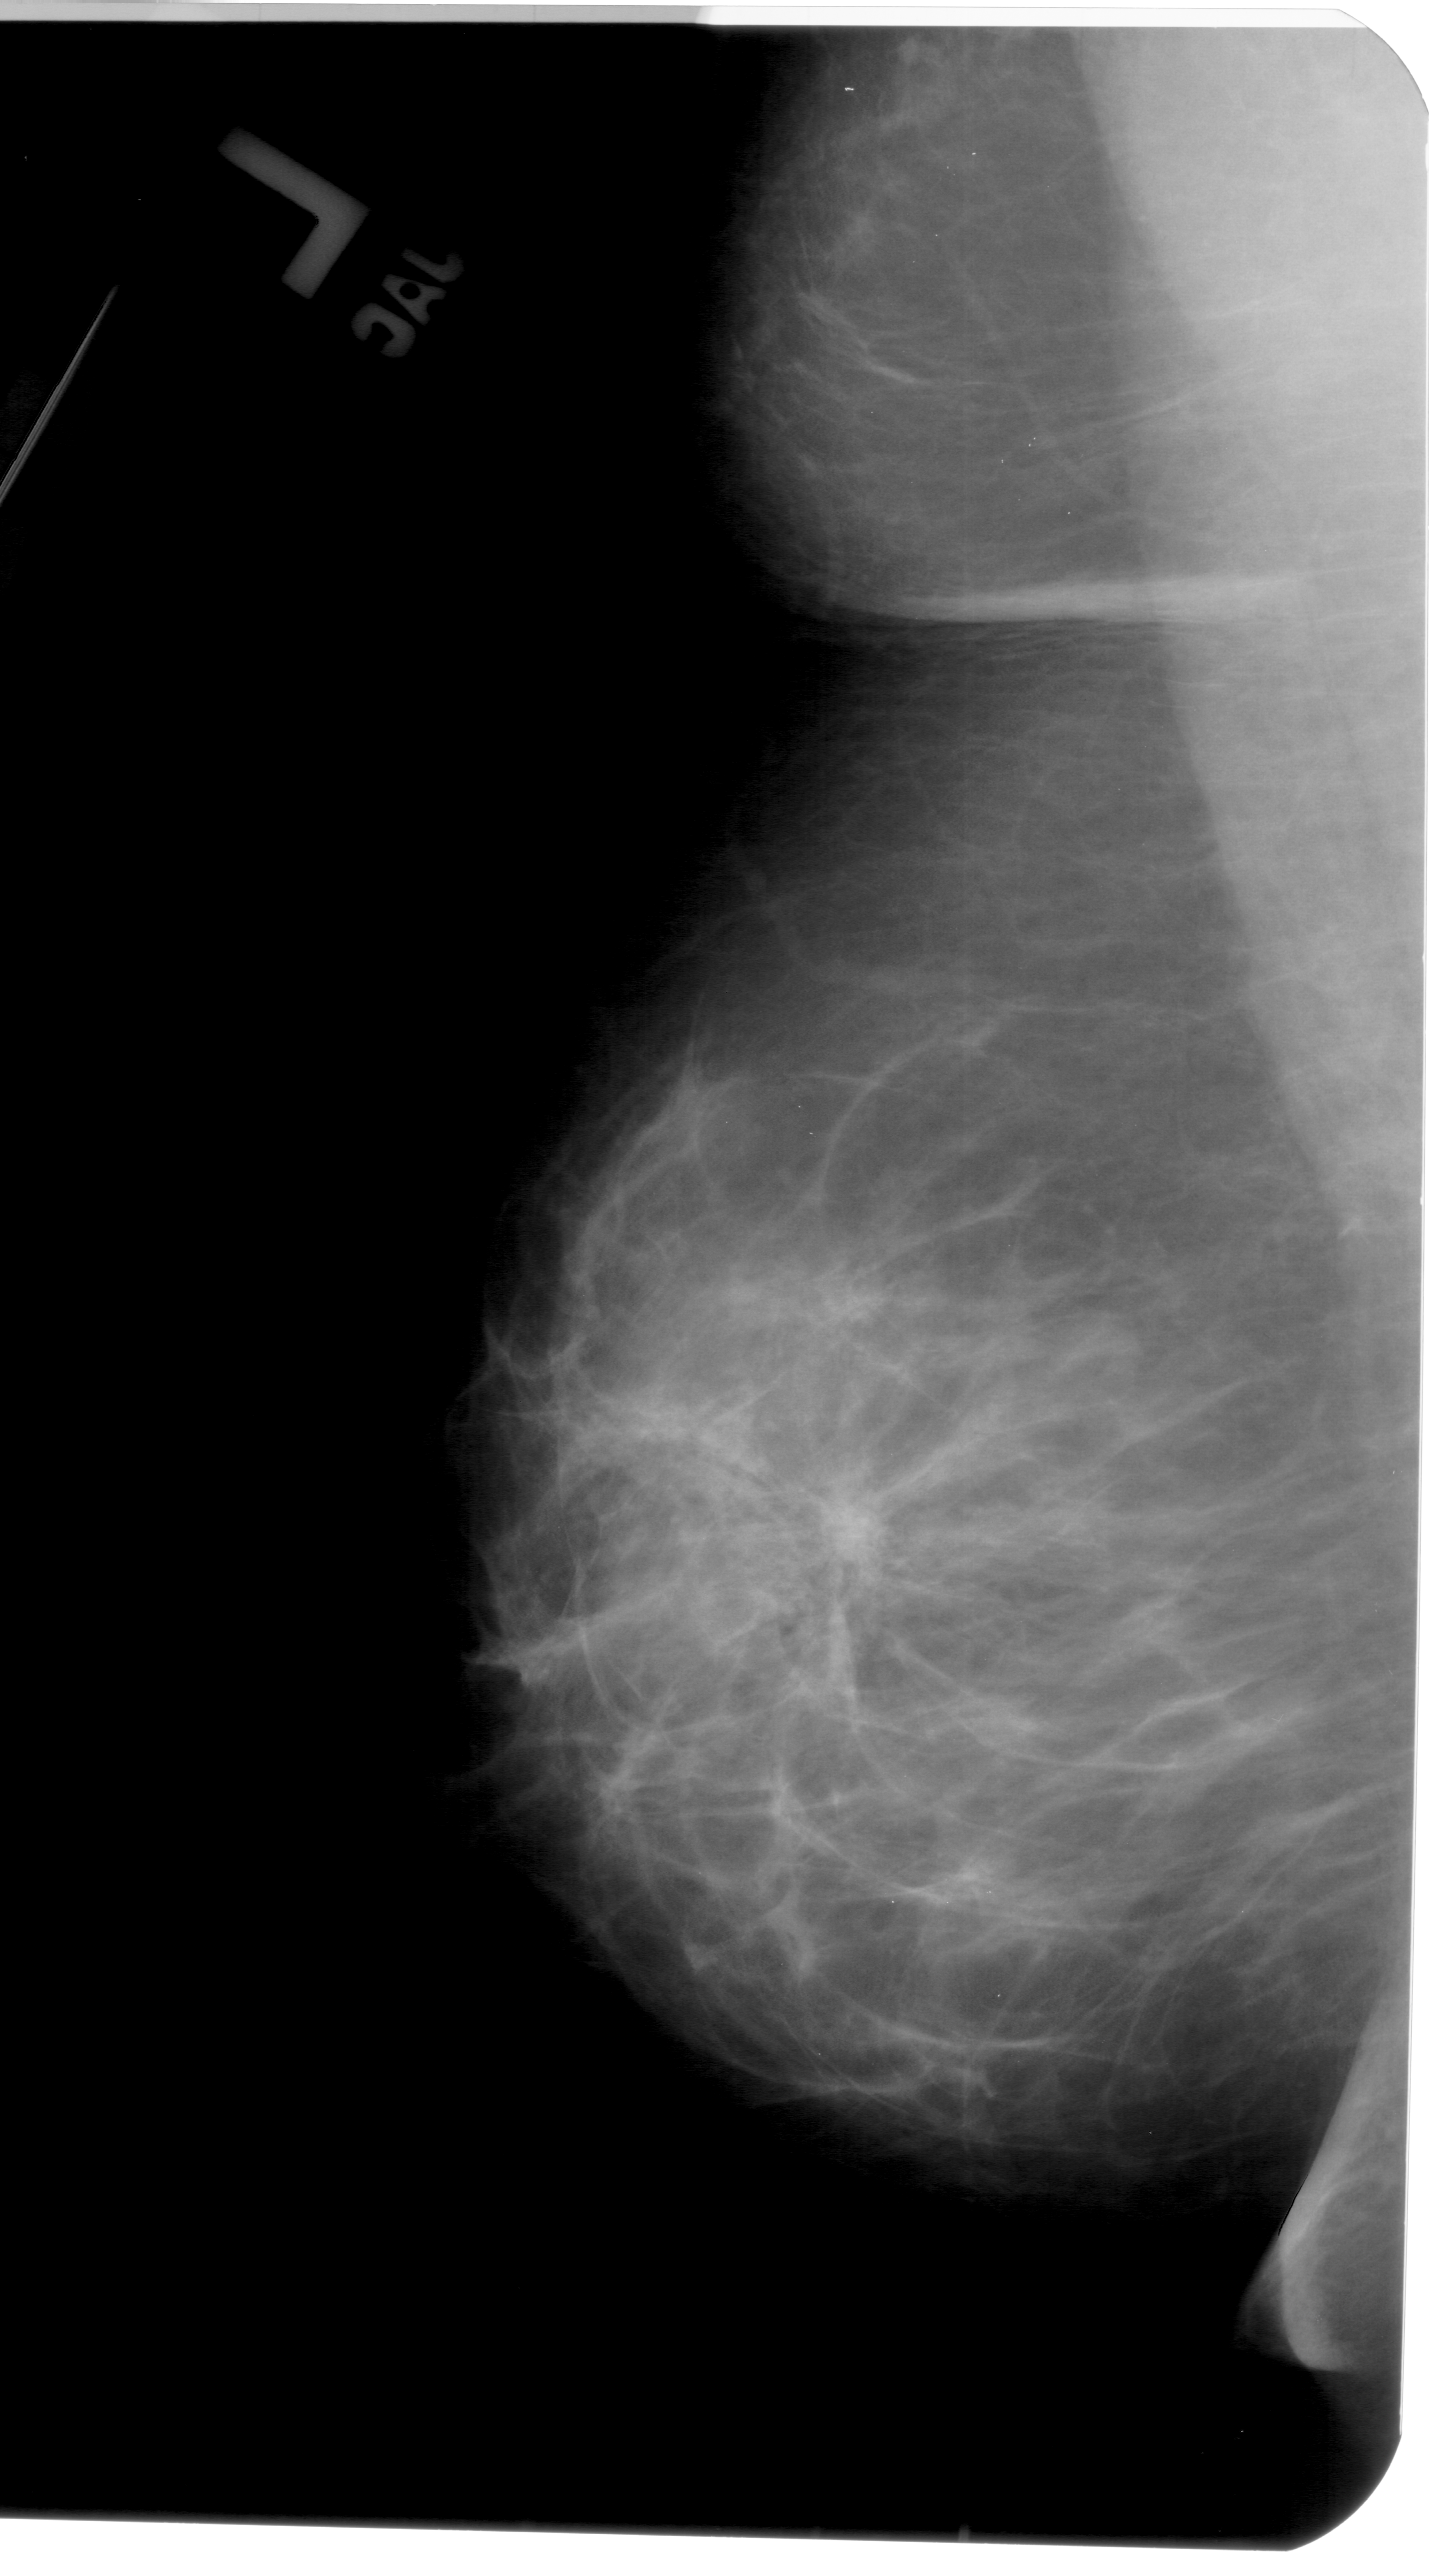
Mammogram (digitized film); left breast; mediolateral oblique (MLO) view; 1429 × 2576 image matrix.
Expert-marked regions of interest on this image (one box per marked abnormality):
- mass, shape architectural distortion, margins ill defined; BI-RADS assessment category 4; pathology result (as recorded, not read from the image): benign: bounding box <775,1433,955,1615> (left, top, right, bottom; pixels)